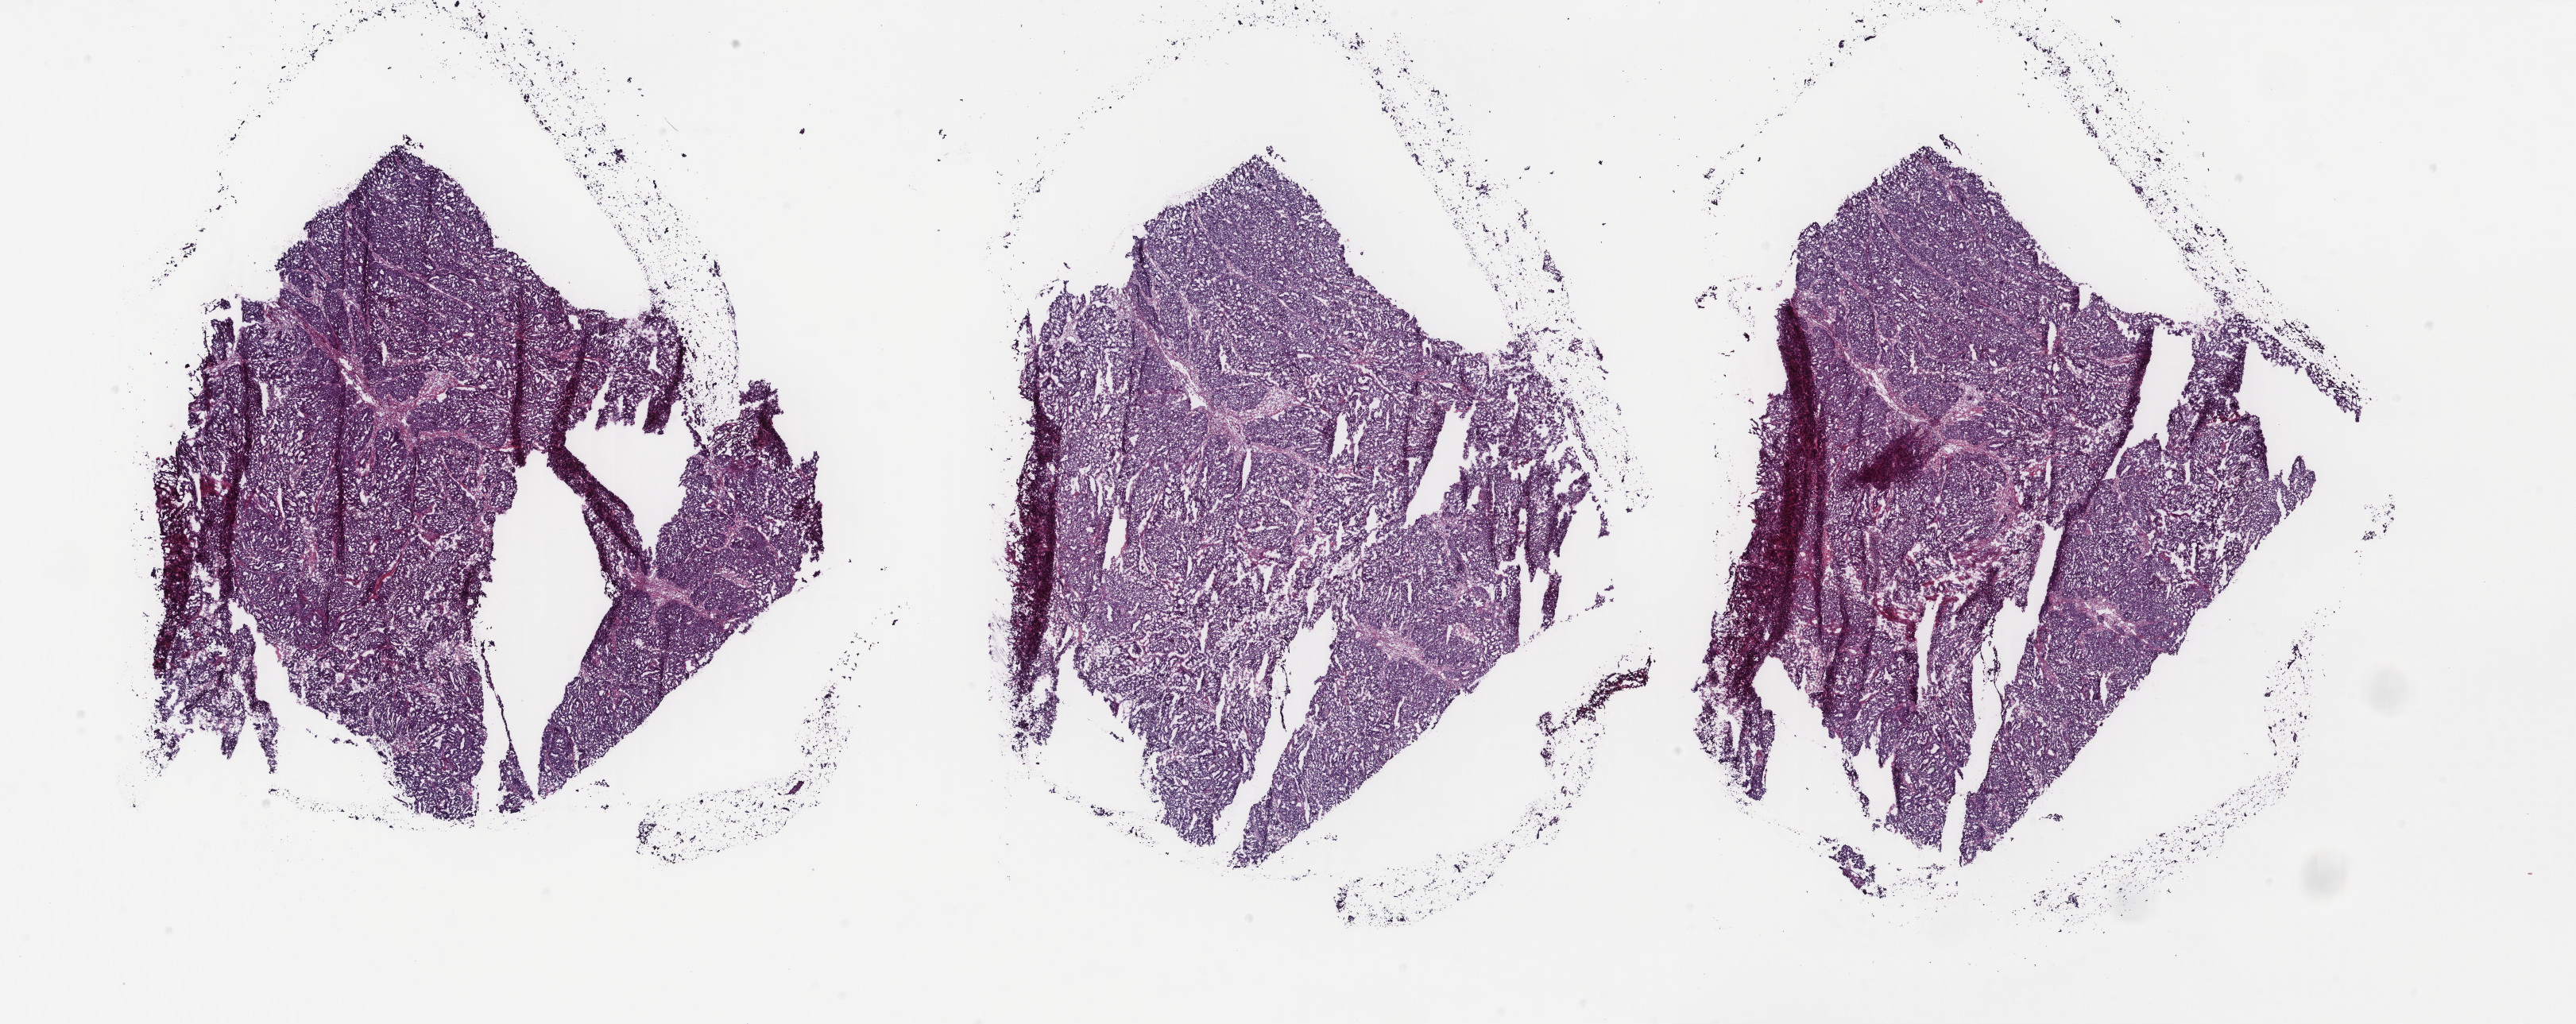
Hematoxylin and eosin (H&E) stained whole-slide image — shown as a low-resolution overview of the whole scanned area (about 25.7 x 10.2 mm, from a 40x scan), frozen section from the top of the tissue portion, primary tumour sample from the uterus. Female patient; age at initial diagnosis 52 years. Histologic grade: G2 (moderately differentiated). Composition of this section per pathologist review: tumour cells 91%, tumour nuclei 95%, normal cells 6%, stromal cells 2%, necrosis 1%. Infiltration values recorded for this section: lymphocyte infiltration 1%, monocyte infiltration 0%, neutrophil infiltration 0%.
Histologic diagnosis: Endometrioid adenocarcinoma, NOS (endometrium). FIGO stage: IB.